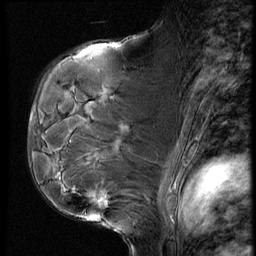
Breast MRI (dynamic contrast-enhanced), one sagittal slice; slice 37 of 60 in the series (ordered by position); dynamic contrast-enhanced series, image 2 of 4 at this slice position (ordered by acquisition); 1.5 T; TE 4.2 ms, TR 9 ms; 2.5 mm slice thickness; 256 × 256 image matrix, field of view 180 × 180 mm. Patient: female, 50 years. From the clinical record (not read from this slice): setting: breast cancer imaged before/during neoadjuvant chemotherapy; receptor status: HR-positive, HER2-negative.
Structures marked on this image (semi-automatic segmentation, software-assisted and operator-edited):
- analysis volume of interest (the breast-tissue region the enhancement analysis was run in; not a lesion): bounding box (x1, y1, x2, y2) in pixels: (48, 109, 135, 230)
- tumour enhancement mask (voxels above the 140 % enhancement threshold inside the analysis volume of interest): (105, 201, 107, 203)